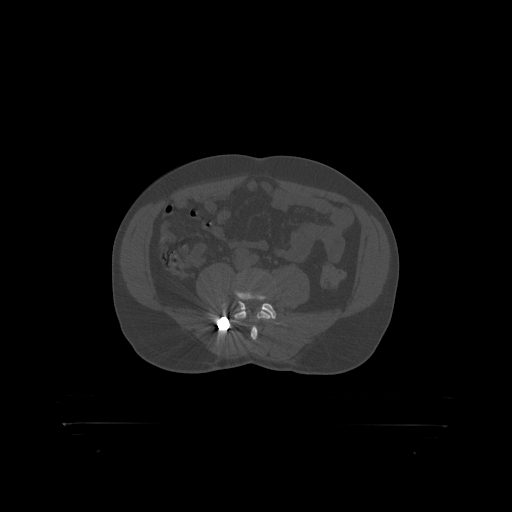
CT including the spine, one axial slice. Position 220 of 399 along the scan axis. 120 kVp. Bone window (W 1800 / L 400 HU). 512 × 512 image matrix, field of view 650 × 650 mm. Patient: male, 46 years. Case-level facts recorded for this patient, not image findings: primary cancer: skin.
Outlined on this slice (semi-automatically segmented with operator editing):
- L4 vertebra: bounding box (x1, y1, x2, y2) in pixels: (235, 310, 272, 319)
- L5 vertebra: (223, 292, 277, 317)